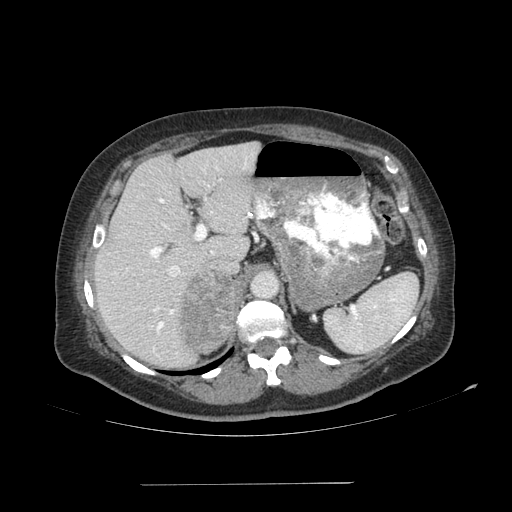
Contrast-enhanced abdominal CT, one axial slice. Slice 72 of 113 in the series (ordered by position). Reconstruction kernel SOFT. 120 kVp. Soft-tissue window (W 400 / L 40 HU). 512 × 512 image matrix. Patient: female, 67 years. From the clinical record (not read from this slice): diagnosis: adrenocortical carcinoma; tumour side: right adrenal; tumour size at pathology: 9.8 cm.
Structures marked on this image (semi-automatically segmented with operator editing):
- mass: bounding box <179,273,238,353> (left, top, right, bottom; pixels)